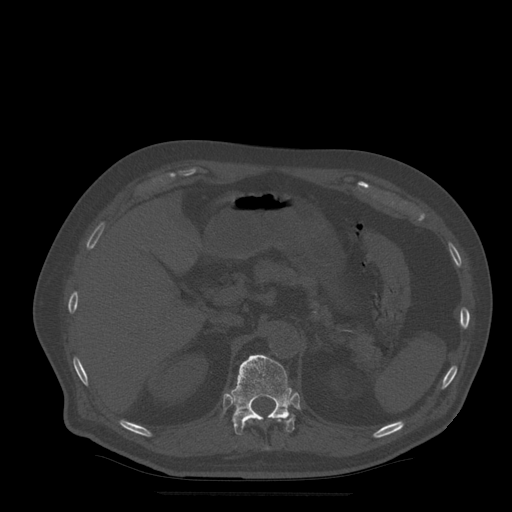
CT including the spine, one axial slice; position 226 of 522 along the scan axis; bone window (W 1800 / L 400 HU); 1.25 mm slice thickness; 512 × 512 image matrix. Patient age 72 years. From the clinical record (not read from this slice): primary cancer: prostate.
Structures marked on this image (semi-automatic segmentation, software-assisted and operator-edited):
- T11 vertebra: bounding box [x1, y1, x2, y2] px = [251, 416, 281, 450]
- T12 vertebra: [231, 355, 295, 435]